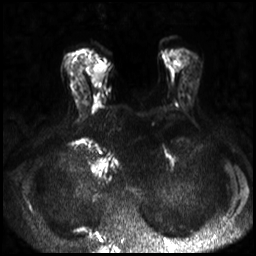
Breast MRI, one axial slice. Diffusion-weighted series; image 2 of 4 stored at this slice position (different b-values; order by instance number). 3 T. 4 mm slice thickness. 256 × 256 image matrix, field of view 320 × 320 mm. Female patient.
Outlined on this slice (outlined manually by an expert reader):
- tumour on diffusion-weighted imaging: bounding box [x1, y1, x2, y2] px = [94, 64, 106, 82]